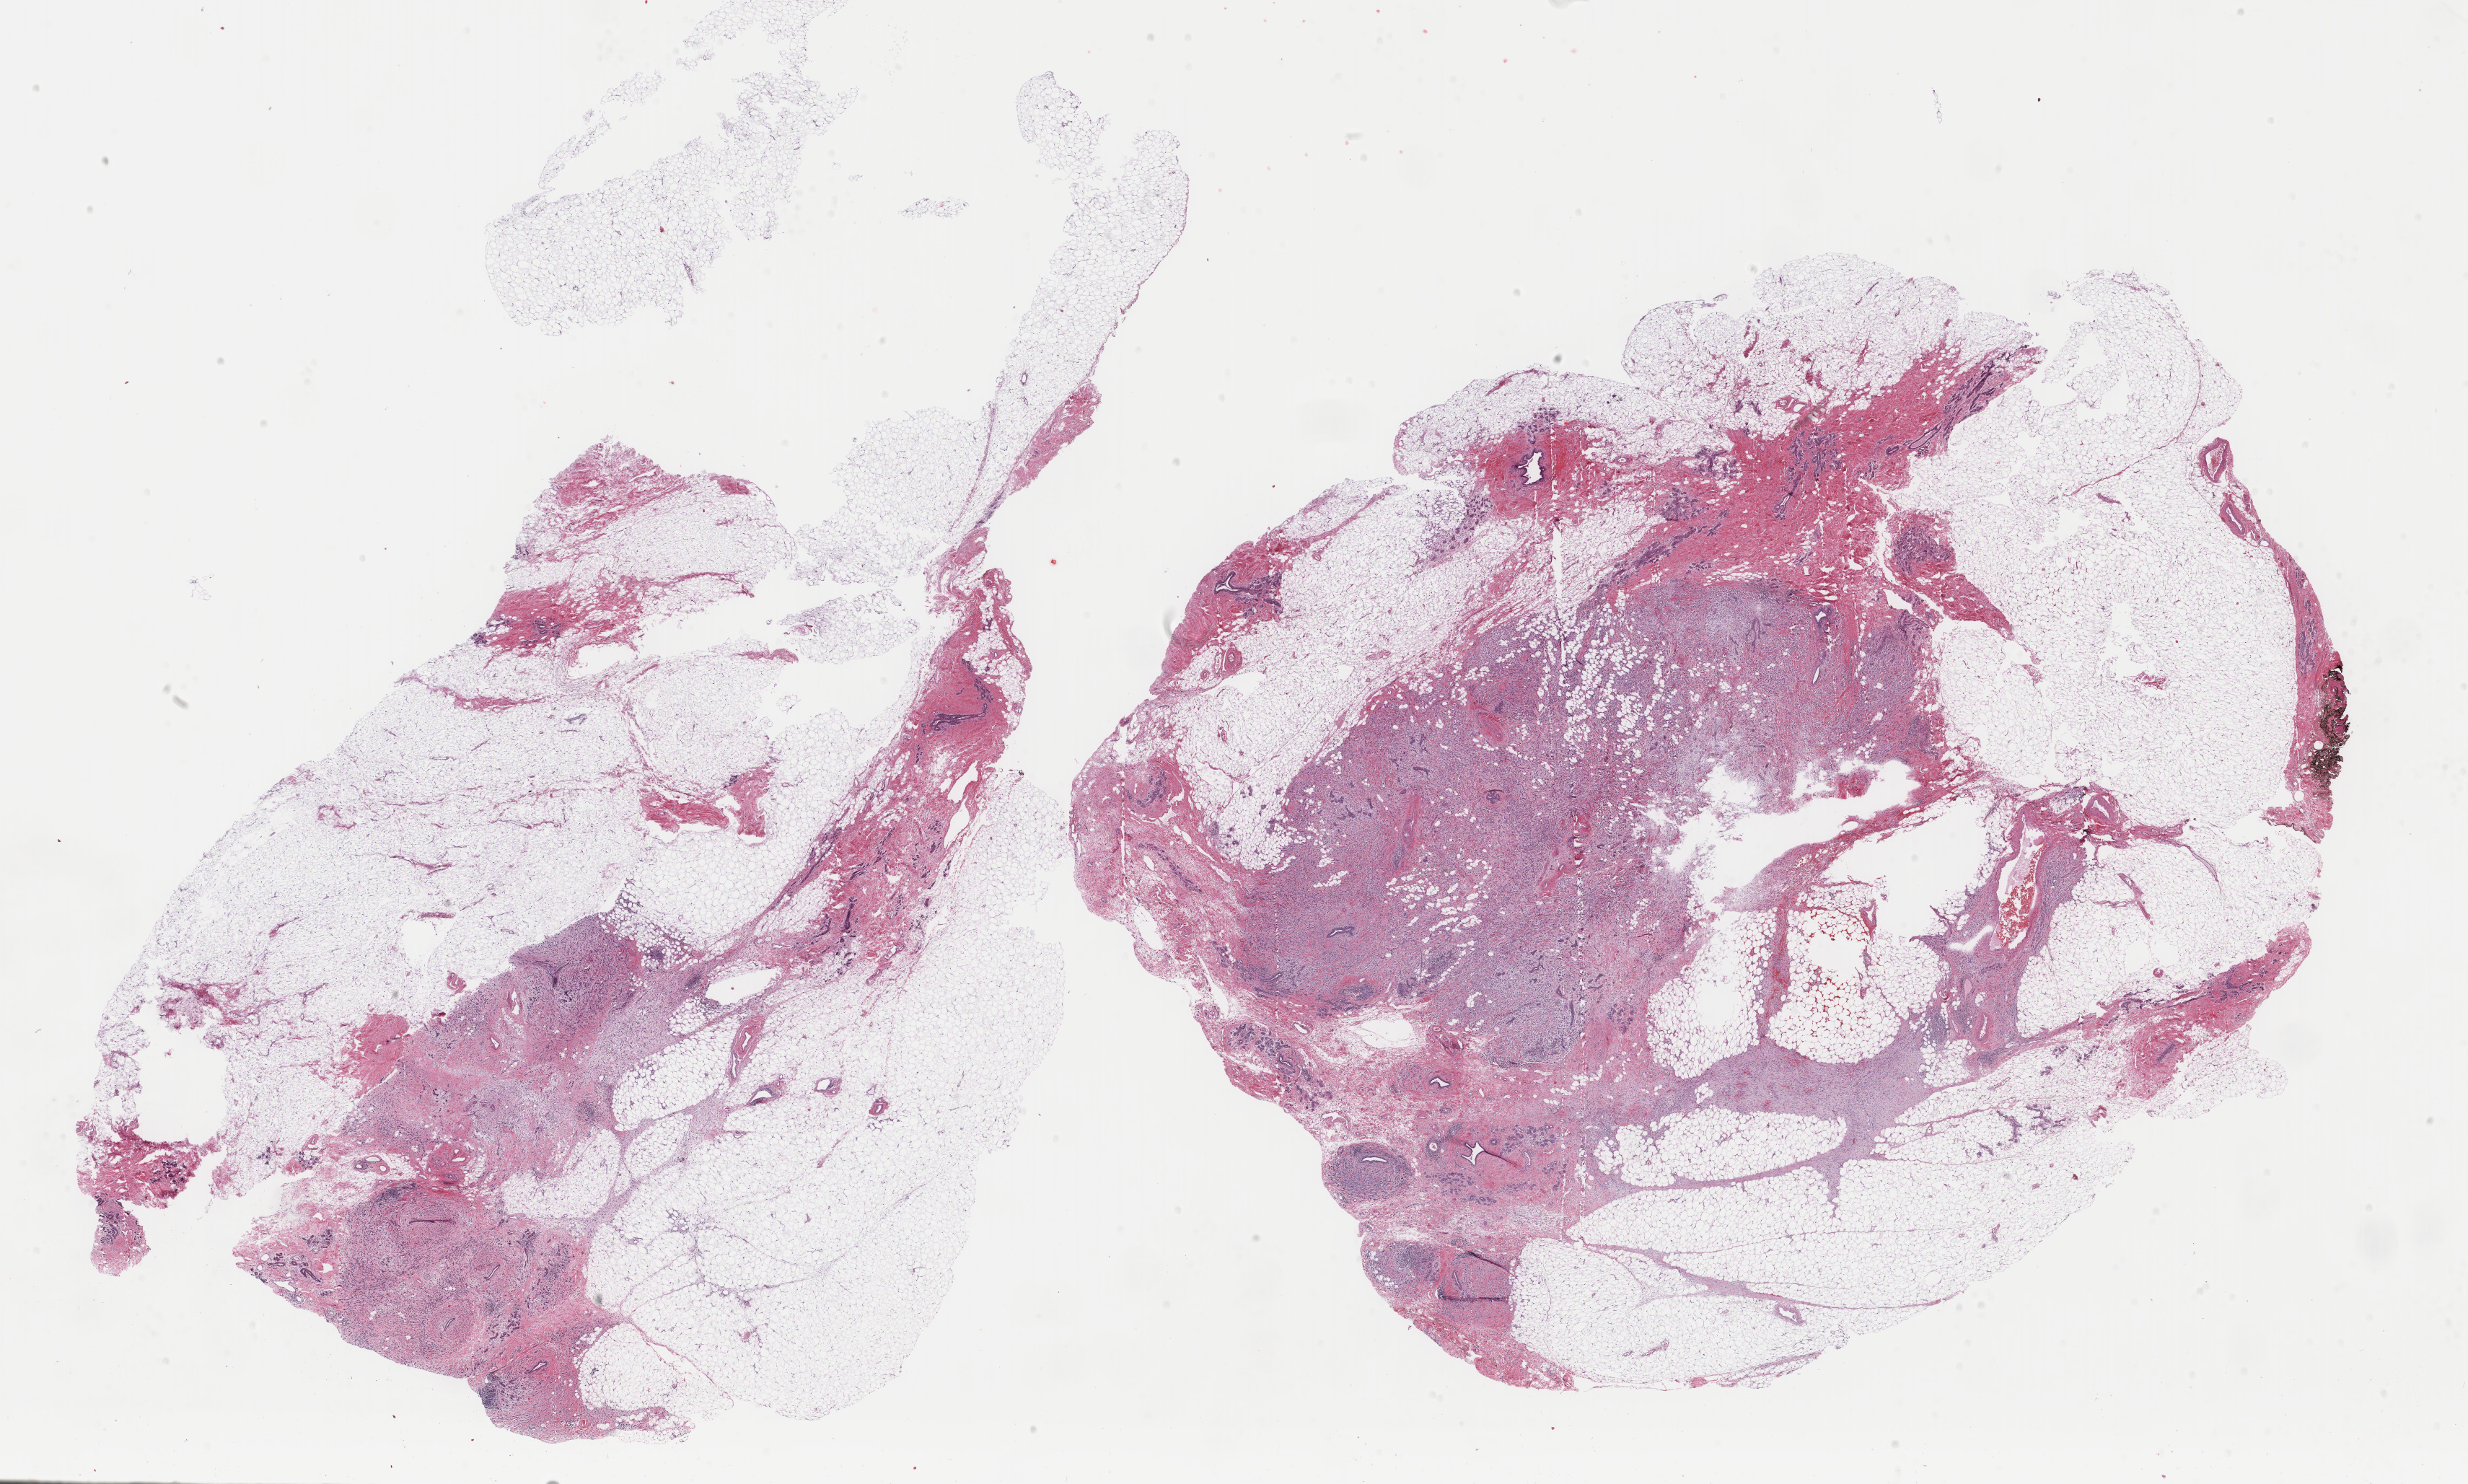
Whole-slide histology image, H&E-stained — low-resolution overview of the scanned area, about 27.2 x 16.3 mm (from a 40x scan), formalin-fixed paraffin-embedded (FFPE) diagnostic section, breast, primary tumour sample. Patient: female, age at initial diagnosis 46 years.
• AJCC pathologic stage: IIB
• histologic diagnosis: Lobular carcinoma, NOS
• TNM: T2 N1 M0
• lymph nodes positive (case pathology): 1 of 16 examined